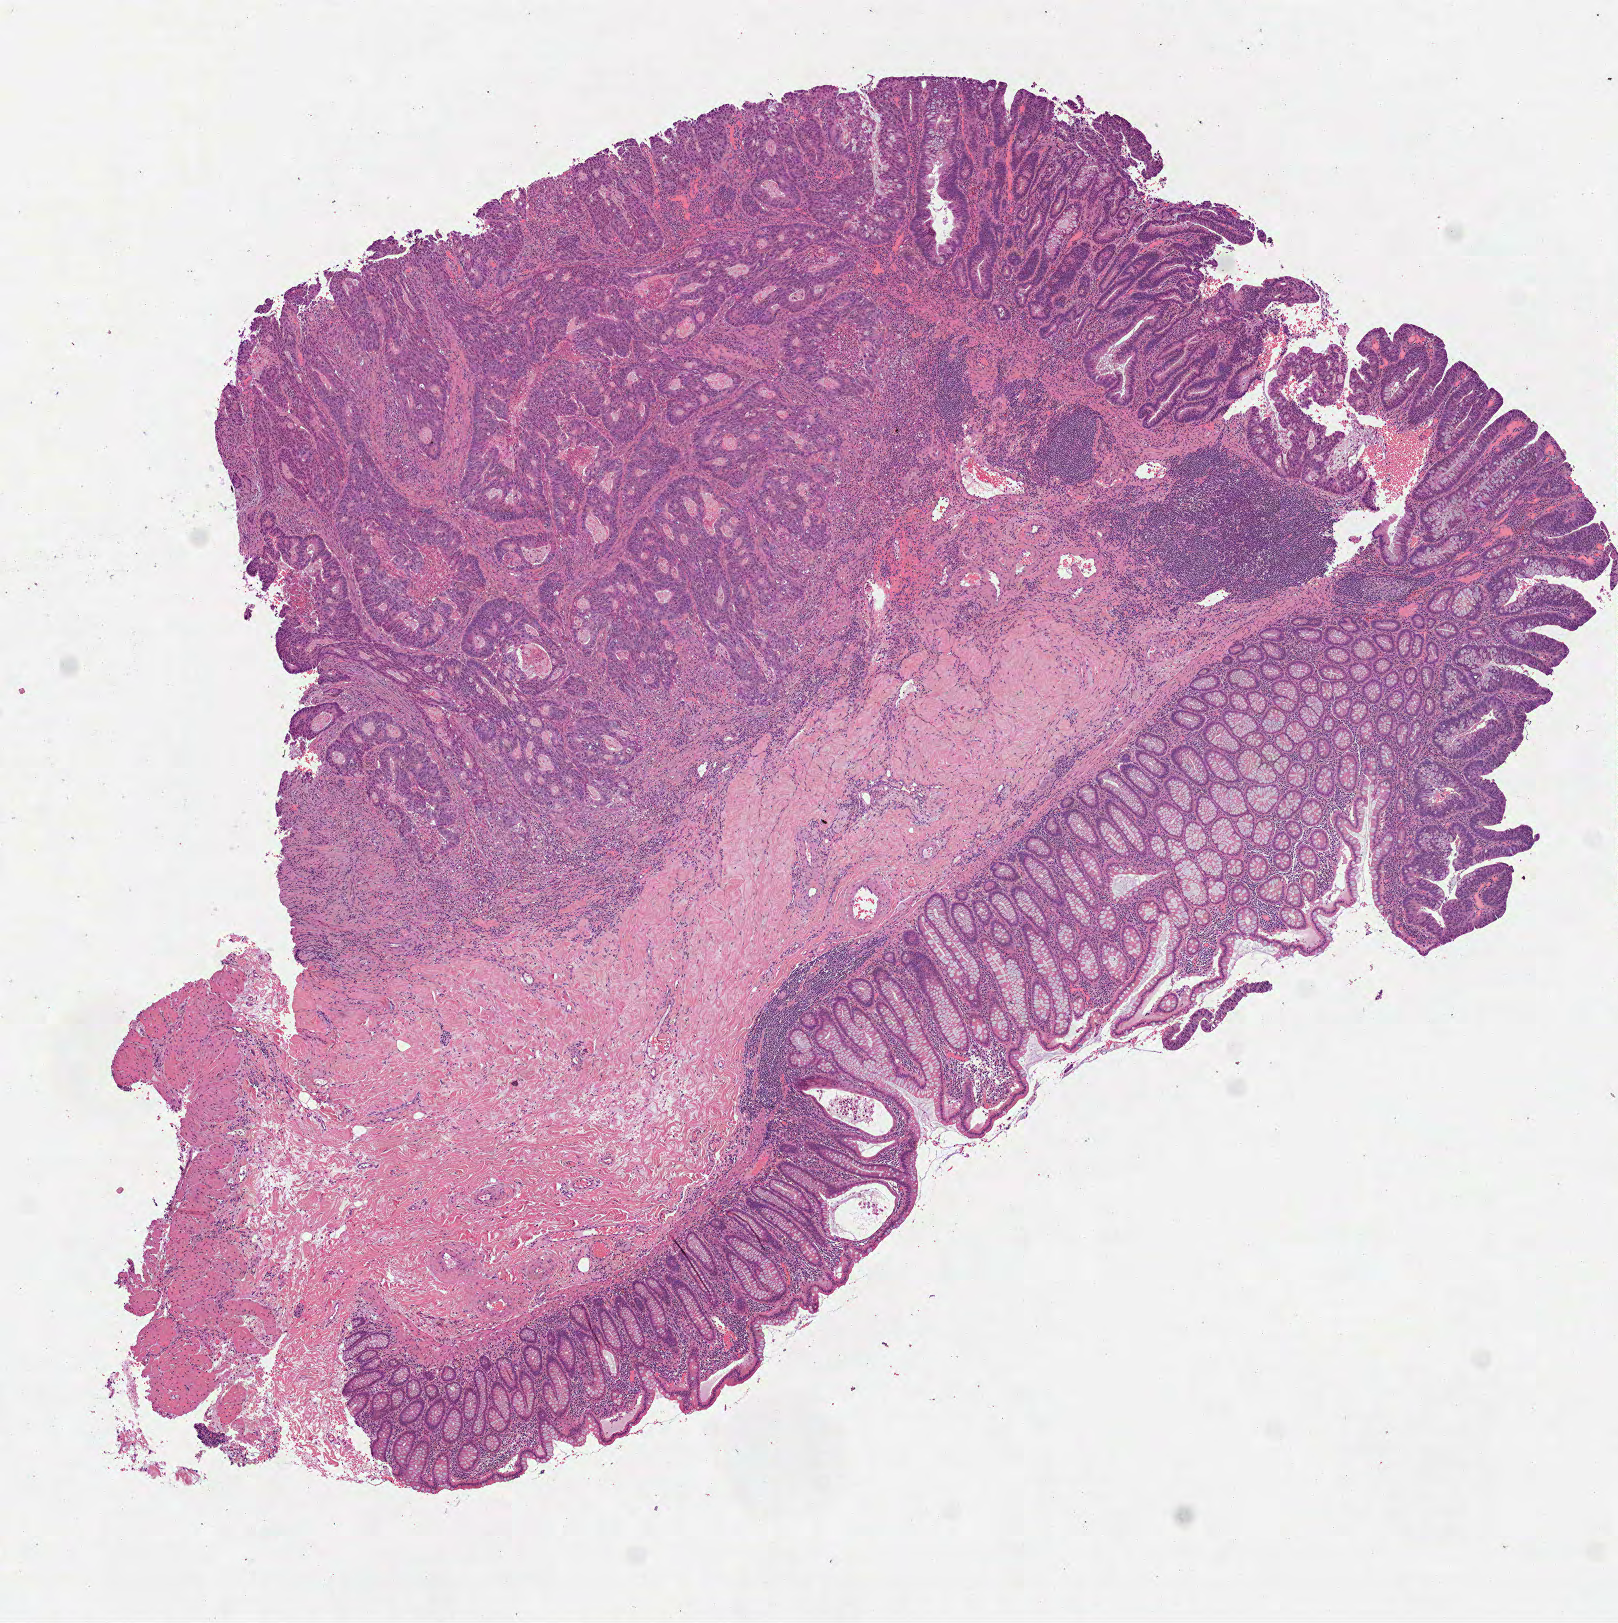
Whole-slide histology image, H&E-stained — whole scanned area (about 6.5 x 6.5 mm) shown as a low-resolution overview. Formalin-fixed paraffin-embedded (FFPE) diagnostic section. Sample: primary tumour, colon. Male patient; age at initial diagnosis 65 years.
• diagnosis: Adenocarcinoma, NOS (ascending colon)